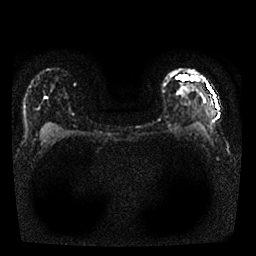
Breast MRI, one axial slice; slice 19 of 25 in the series (ordered by position); diffusion-weighted series; image 2 of 4 stored at this slice position (different b-values; order by instance number); 1.5 T; 4 mm slice thickness; 256 × 256 image matrix, field of view 310 × 310 mm. Female patient.
Annotated regions visible in this slice (manually delineated by an expert):
- tumour on diffusion-weighted imaging: bounding box [x1, y1, x2, y2] px = [173, 129, 177, 132]